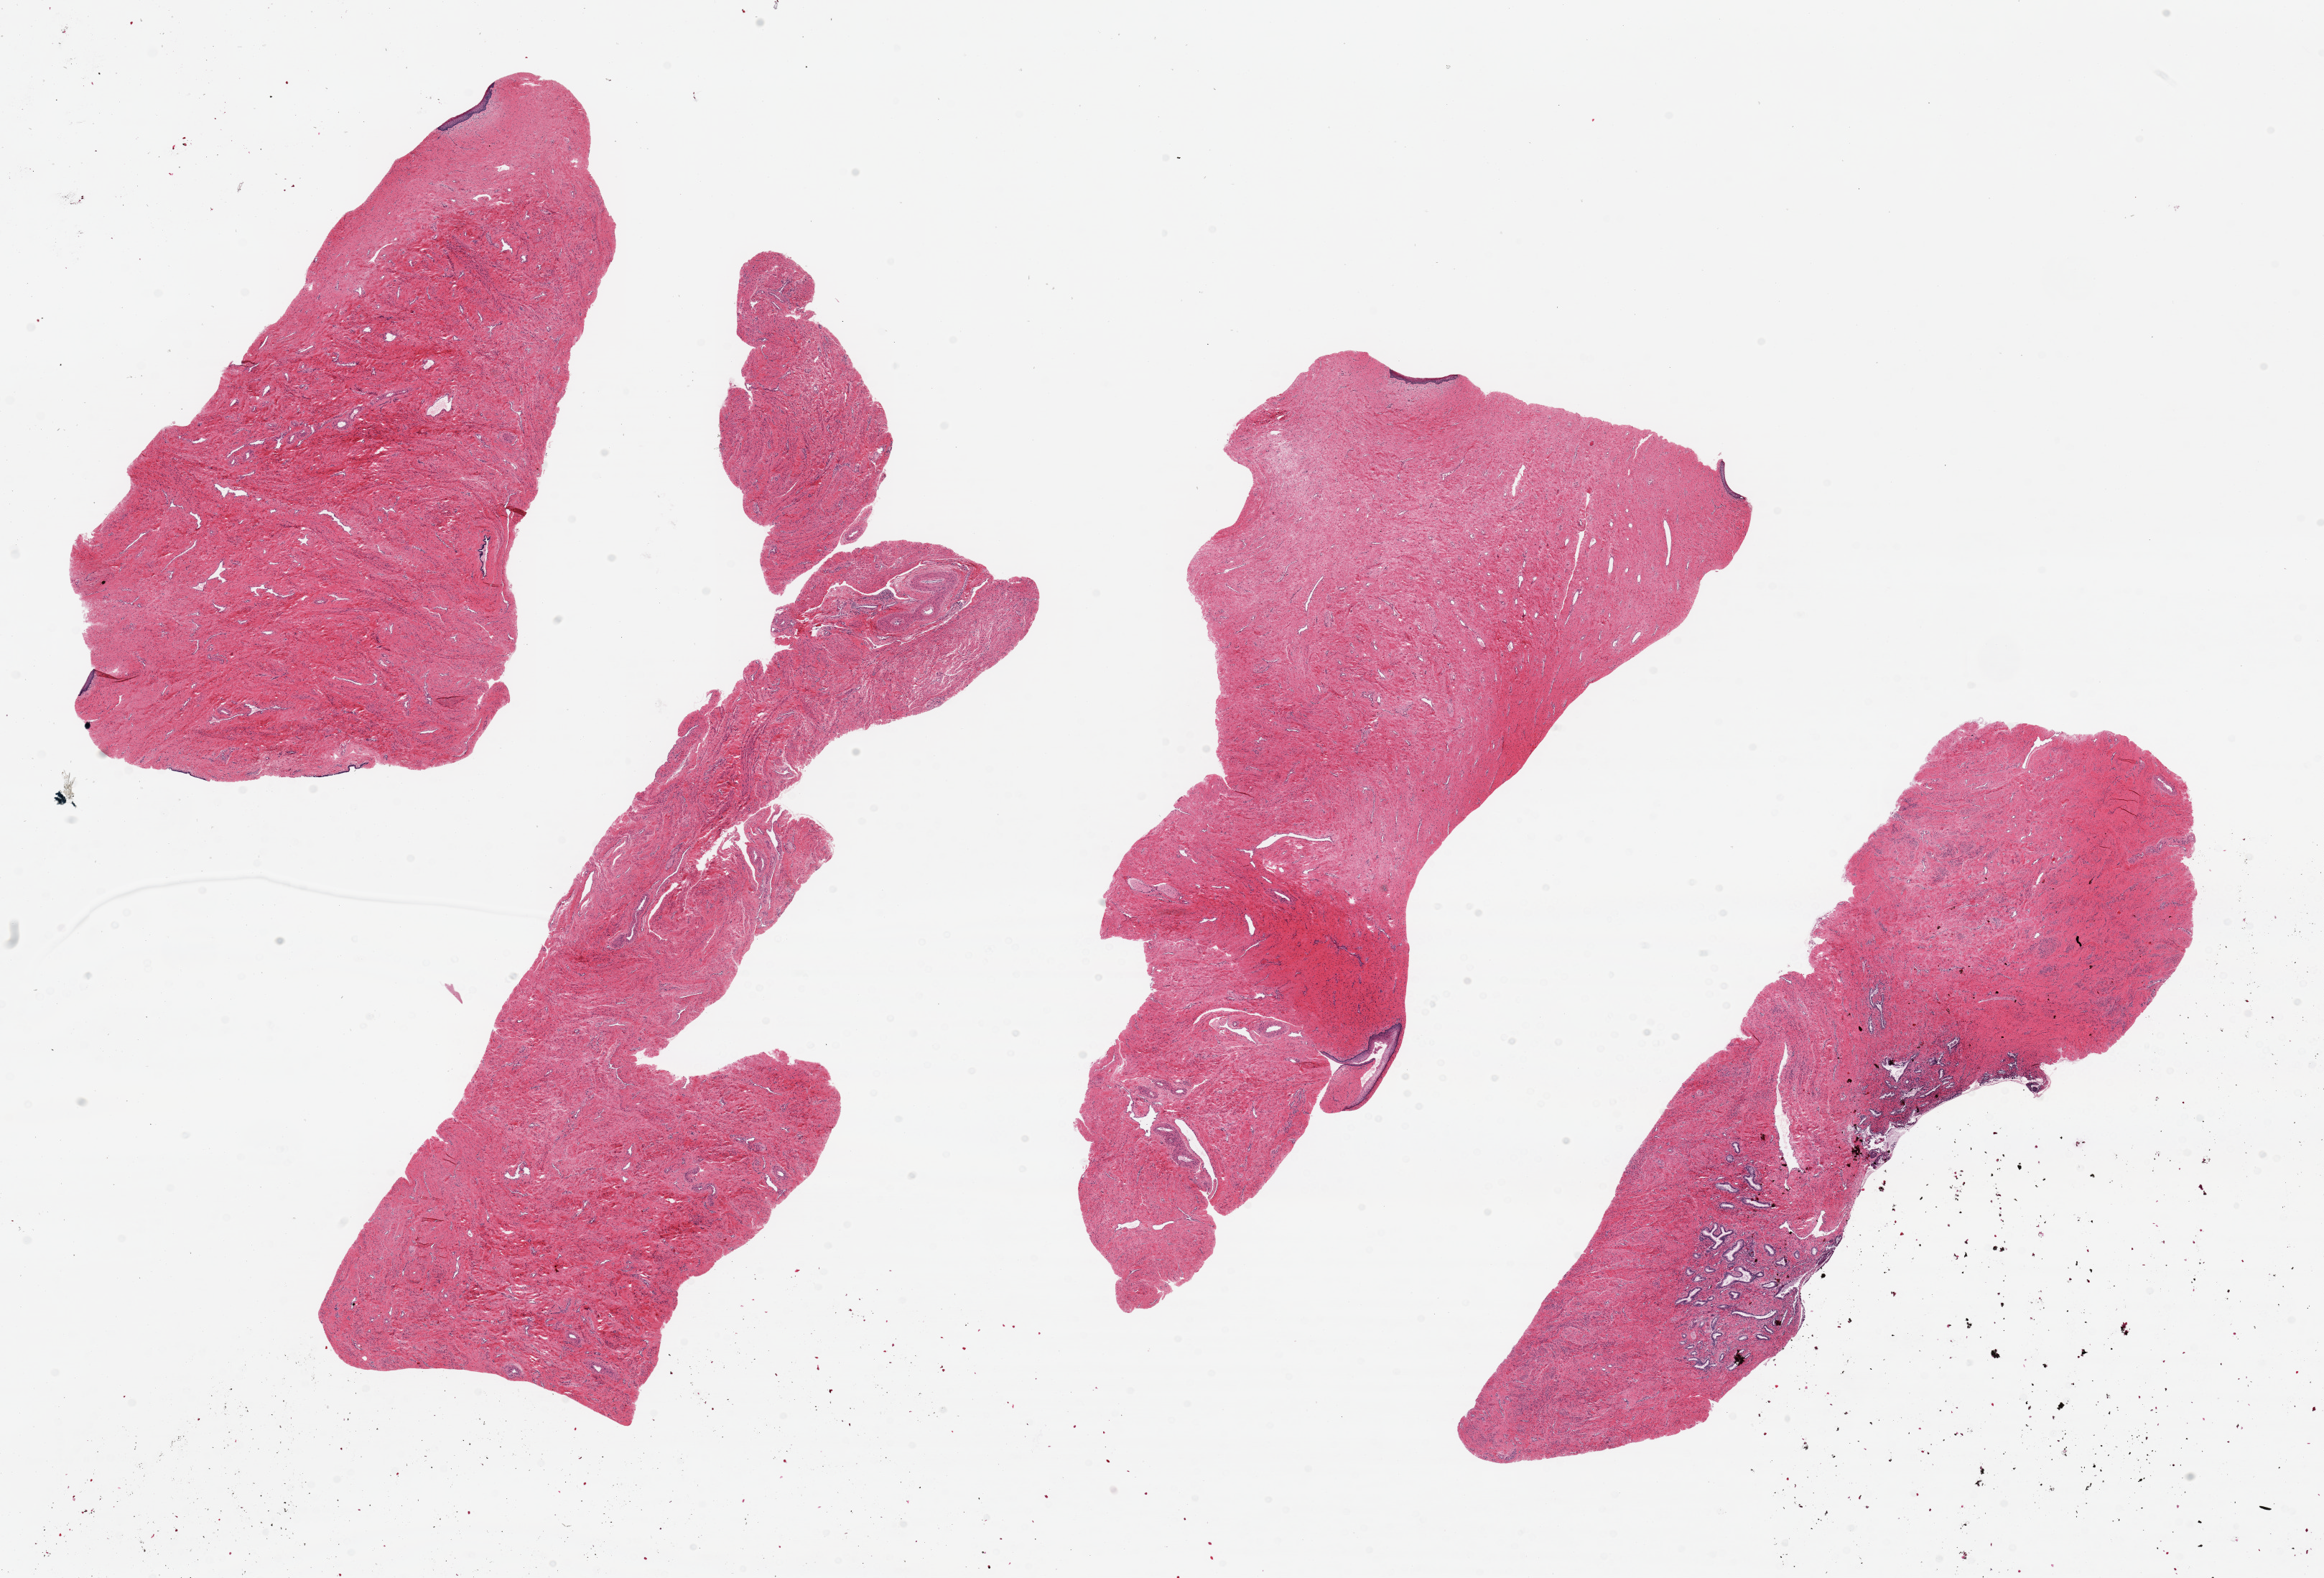
Digitized H&E-stained section, shown as a low-resolution overview of the whole scanned area (about 25.6 x 17.4 mm, acquisition: 20x scan); PAXgene-fixed, paraffin-embedded tissue; target tissue: endocervix; tissue donor sample.
Reviewer comment on this tissue sample: 4 ~10x3.4mm aliquots. Mixed endo & ectocervical mucosa (trace amounts).